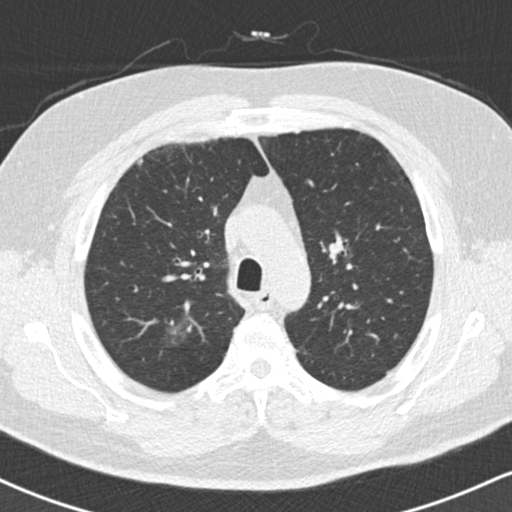
Chest CT (low-dose screening protocol), one axial image, second screening round (one year after baseline), lung window (W 1500 / L -600 HU), 2 mm slice thickness, standard (soft-tissue) reconstruction kernel (B30f). Male participant, aged 59 years at enrolment.
• Expert reader's lesion annotation, bounding box <153,301,209,360> (left, top, right, bottom; pixels).
• Reader record for this screening exam (exam-level; its link to the box is not recorded): non-calcified nodule or mass ≥4 mm, right upper lobe, 18 × 16 mm, ground glass attenuation, pre-existing on the prior screen: yes.
• Participant outcome: lung cancer diagnosed 60 days after this screen — bronchiolo-alveolar adenocarcinoma, NOS, right lower lobe, stage IA (AJCC 6th edition), 15 mm at pathology.